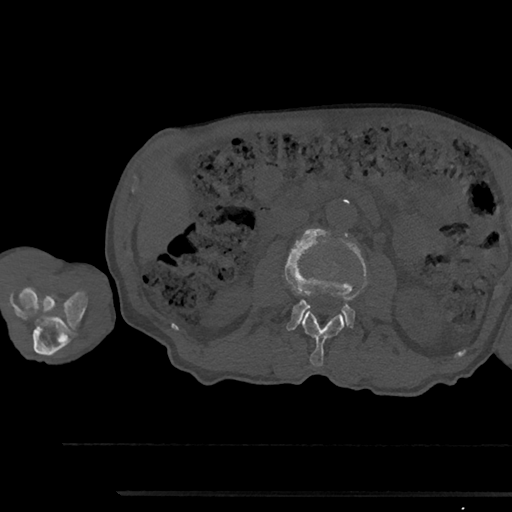
CT including the spine, one axial slice; slice 527 of 797 in the series (ordered by position); reconstruction kernel Br40s/3; 120 kVp; bone window (W 1800 / L 400 HU); 512 × 512 image matrix, field of view 367 × 367 mm. Male patient, age 79 years. Case-level facts recorded for this patient, not image findings: primary cancer: prostate.
Structures marked on this image (semi-automatic segmentation, software-assisted and operator-edited):
- L2 vertebra: box from (x=301, y=311) to (x=345, y=366) px
- L3 vertebra: (x=284, y=229)–(x=367, y=330)